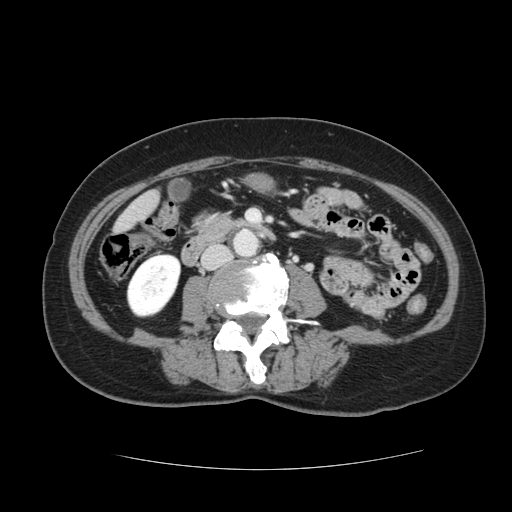
Contrast-enhanced abdominal CT, one axial slice. 120 kVp. Intravenous contrast given. Soft-tissue window (W 400 / L 40 HU). 2.5 mm slice thickness. 512 × 512 image matrix. Female patient, age 67 years. Case-level facts recorded for this patient, not image findings: diagnosis: colorectal cancer liver metastases, imaged before liver resection; multiple liver metastases: yes; largest metastasis: 3 cm; chemotherapy before resection: no.
Structures marked on this image (manually delineated by an expert):
- liver: bounding box [x1, y1, x2, y2] px = [117, 192, 158, 231]
- planned liver remnant (the part of the liver to remain after resection): [117, 206, 144, 231]